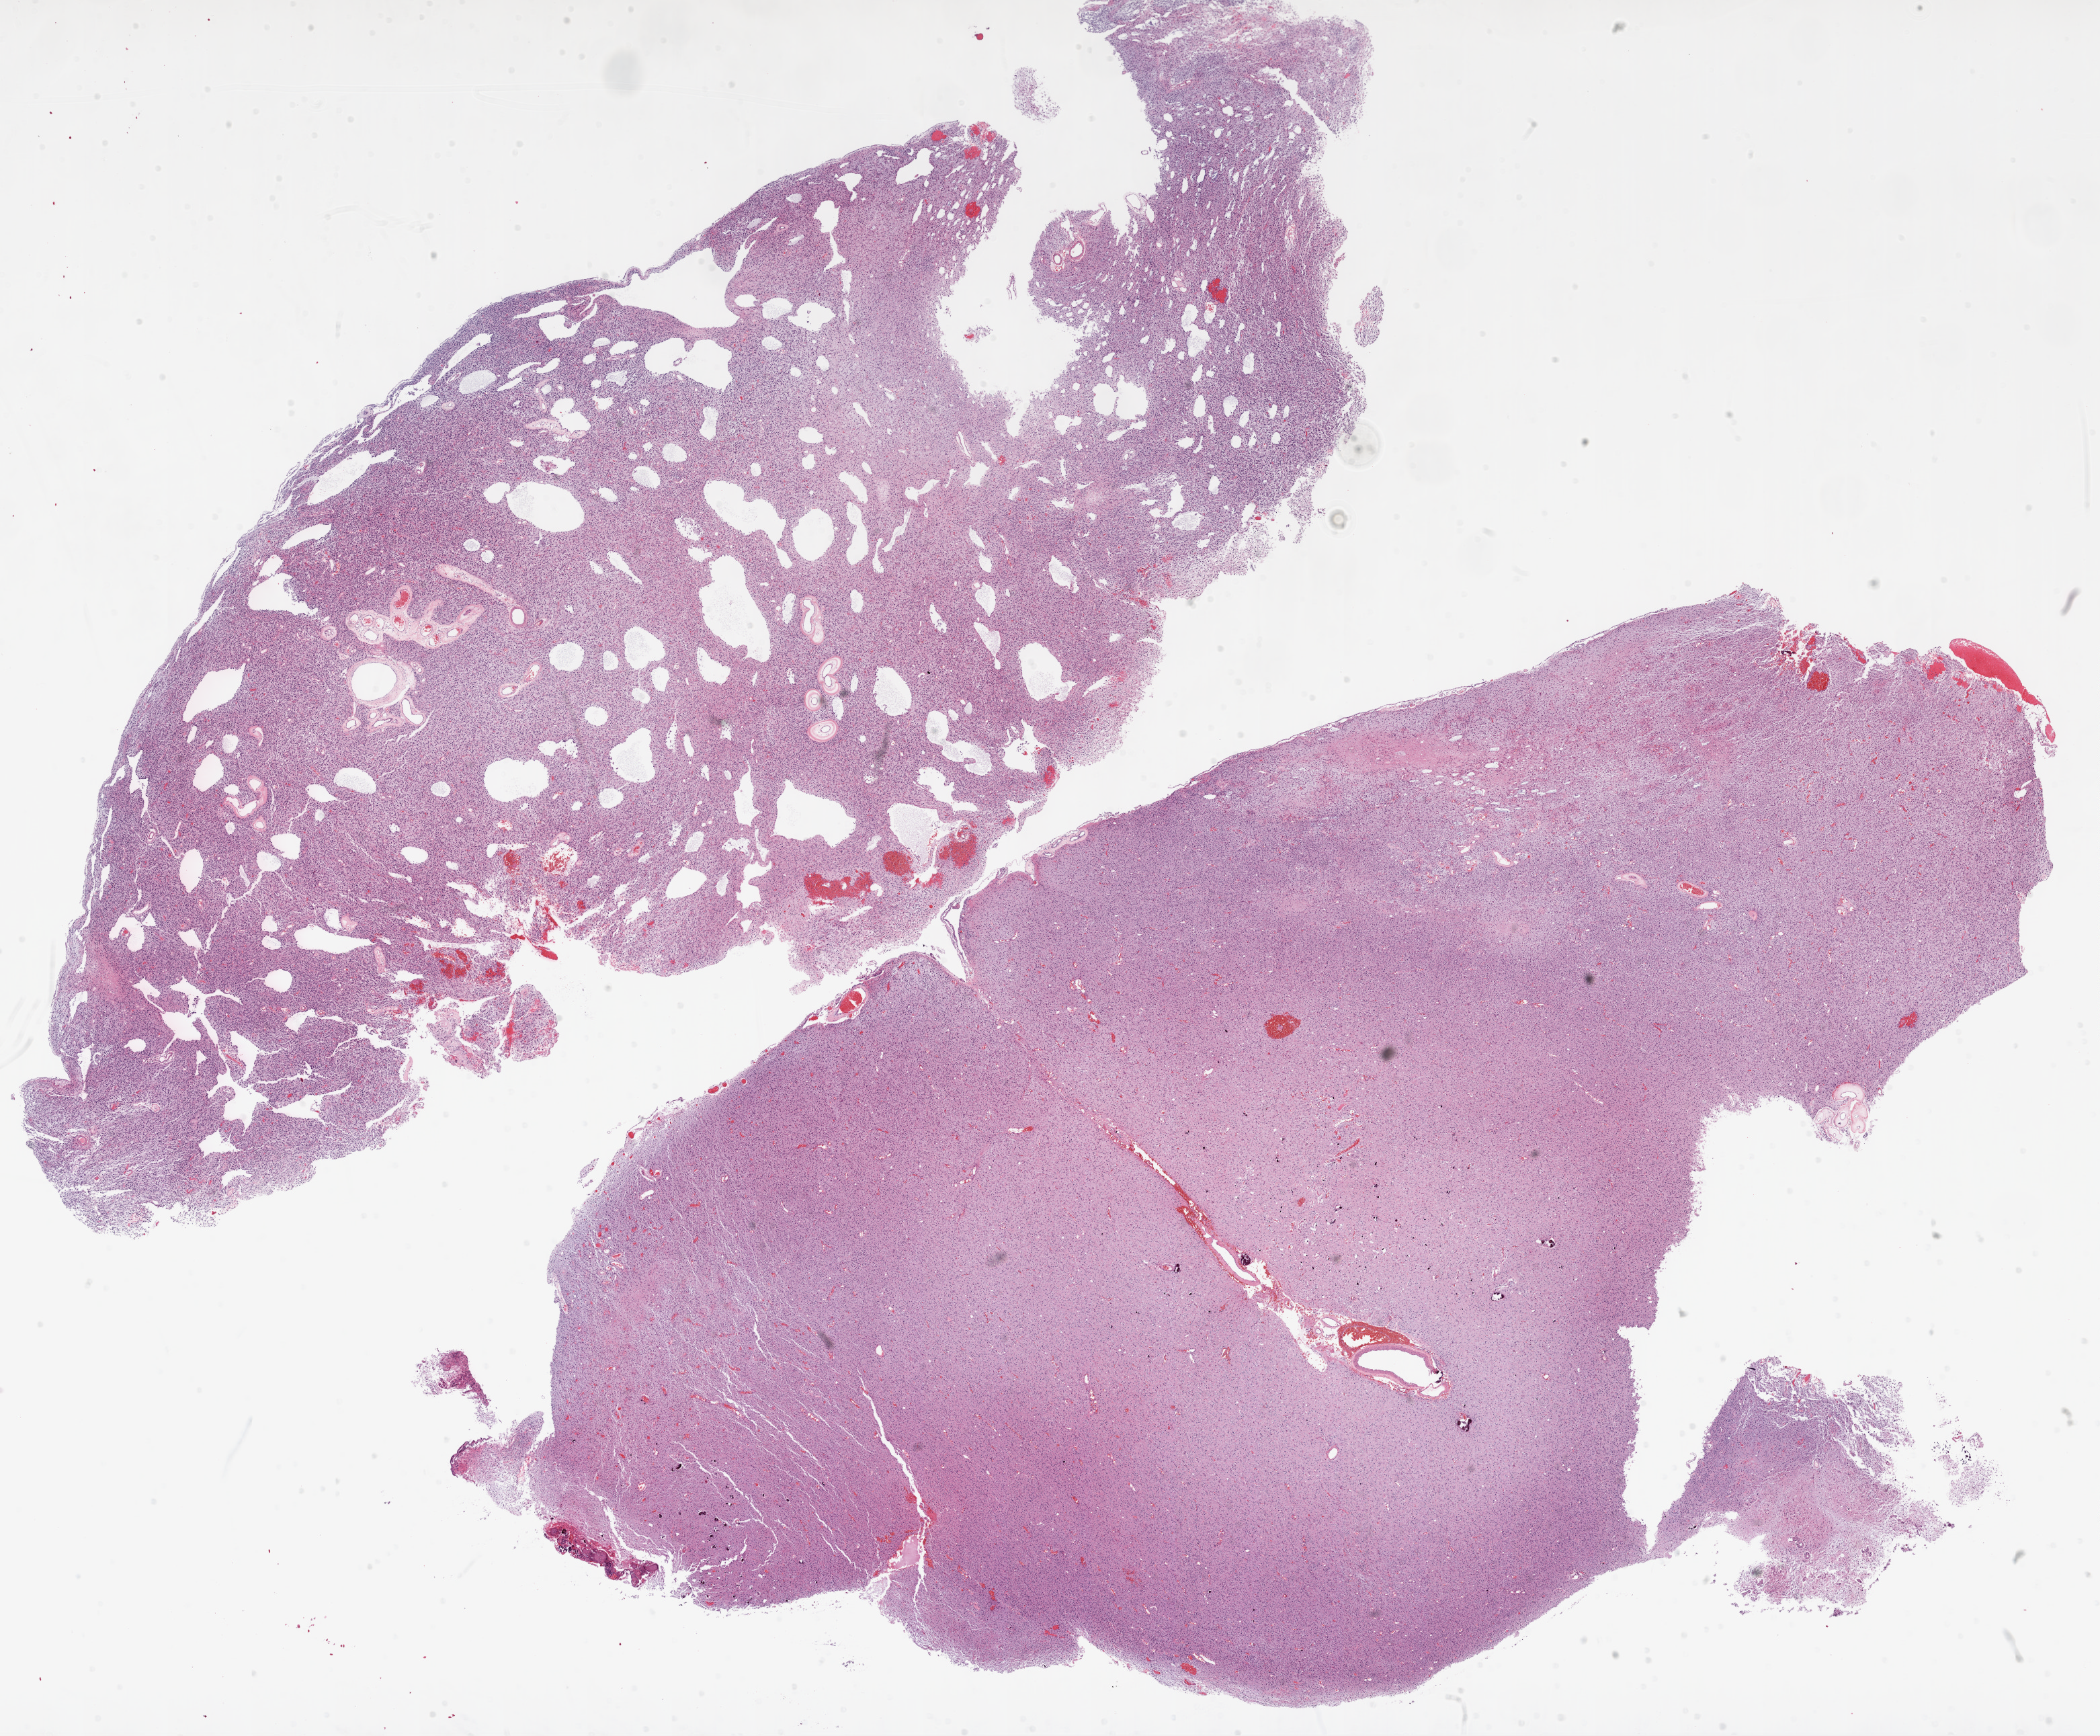
Digitized H&E tissue section (whole slide) — low-resolution overview of the scanned area, about 25.1 x 20.7 mm. Formalin-fixed paraffin-embedded (FFPE) diagnostic section. Primary tumour sample from the brain. Patient: male, age at initial diagnosis 54 years.
Histologic diagnosis: Glioblastoma.